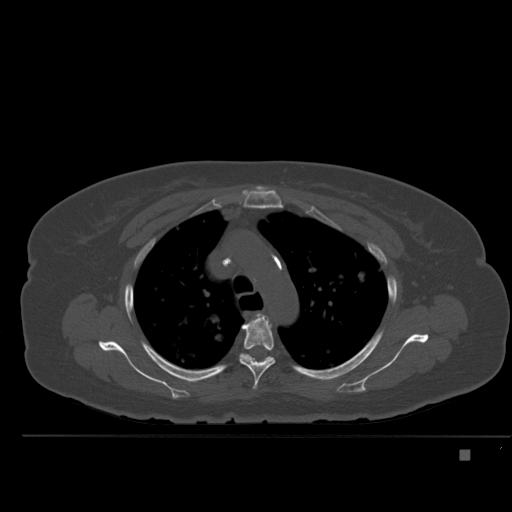
CT including the spine, one axial slice; position 365 of 477 along the scan axis; bone window (W 1800 / L 400 HU); 512 × 512 image matrix, field of view 422 × 422 mm. Patient: female, 74 years. From the clinical record (not read from this slice): primary cancer: colon.
Structures marked on this image (semi-automatic segmentation, software-assisted and operator-edited):
- T4 vertebra: bounding box [x1, y1, x2, y2] px = [239, 315, 275, 390]
- T5 vertebra: [242, 354, 273, 361]